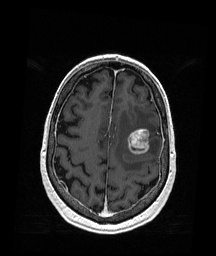
Brain MRI from a brain-tumour surgery series, one axial slice; position 54 of 176 along the scan axis; T1-weighted post-contrast; 1 mm slice thickness; 216 × 256 image matrix, field of view 211 × 250 mm. From the clinical record (not read from this slice): histopathology: Metastatic Melanoma.
Structures marked on this image (expert manual segmentation):
- tumour: bounding box (x1, y1, x2, y2) in pixels: (127, 129, 150, 155)